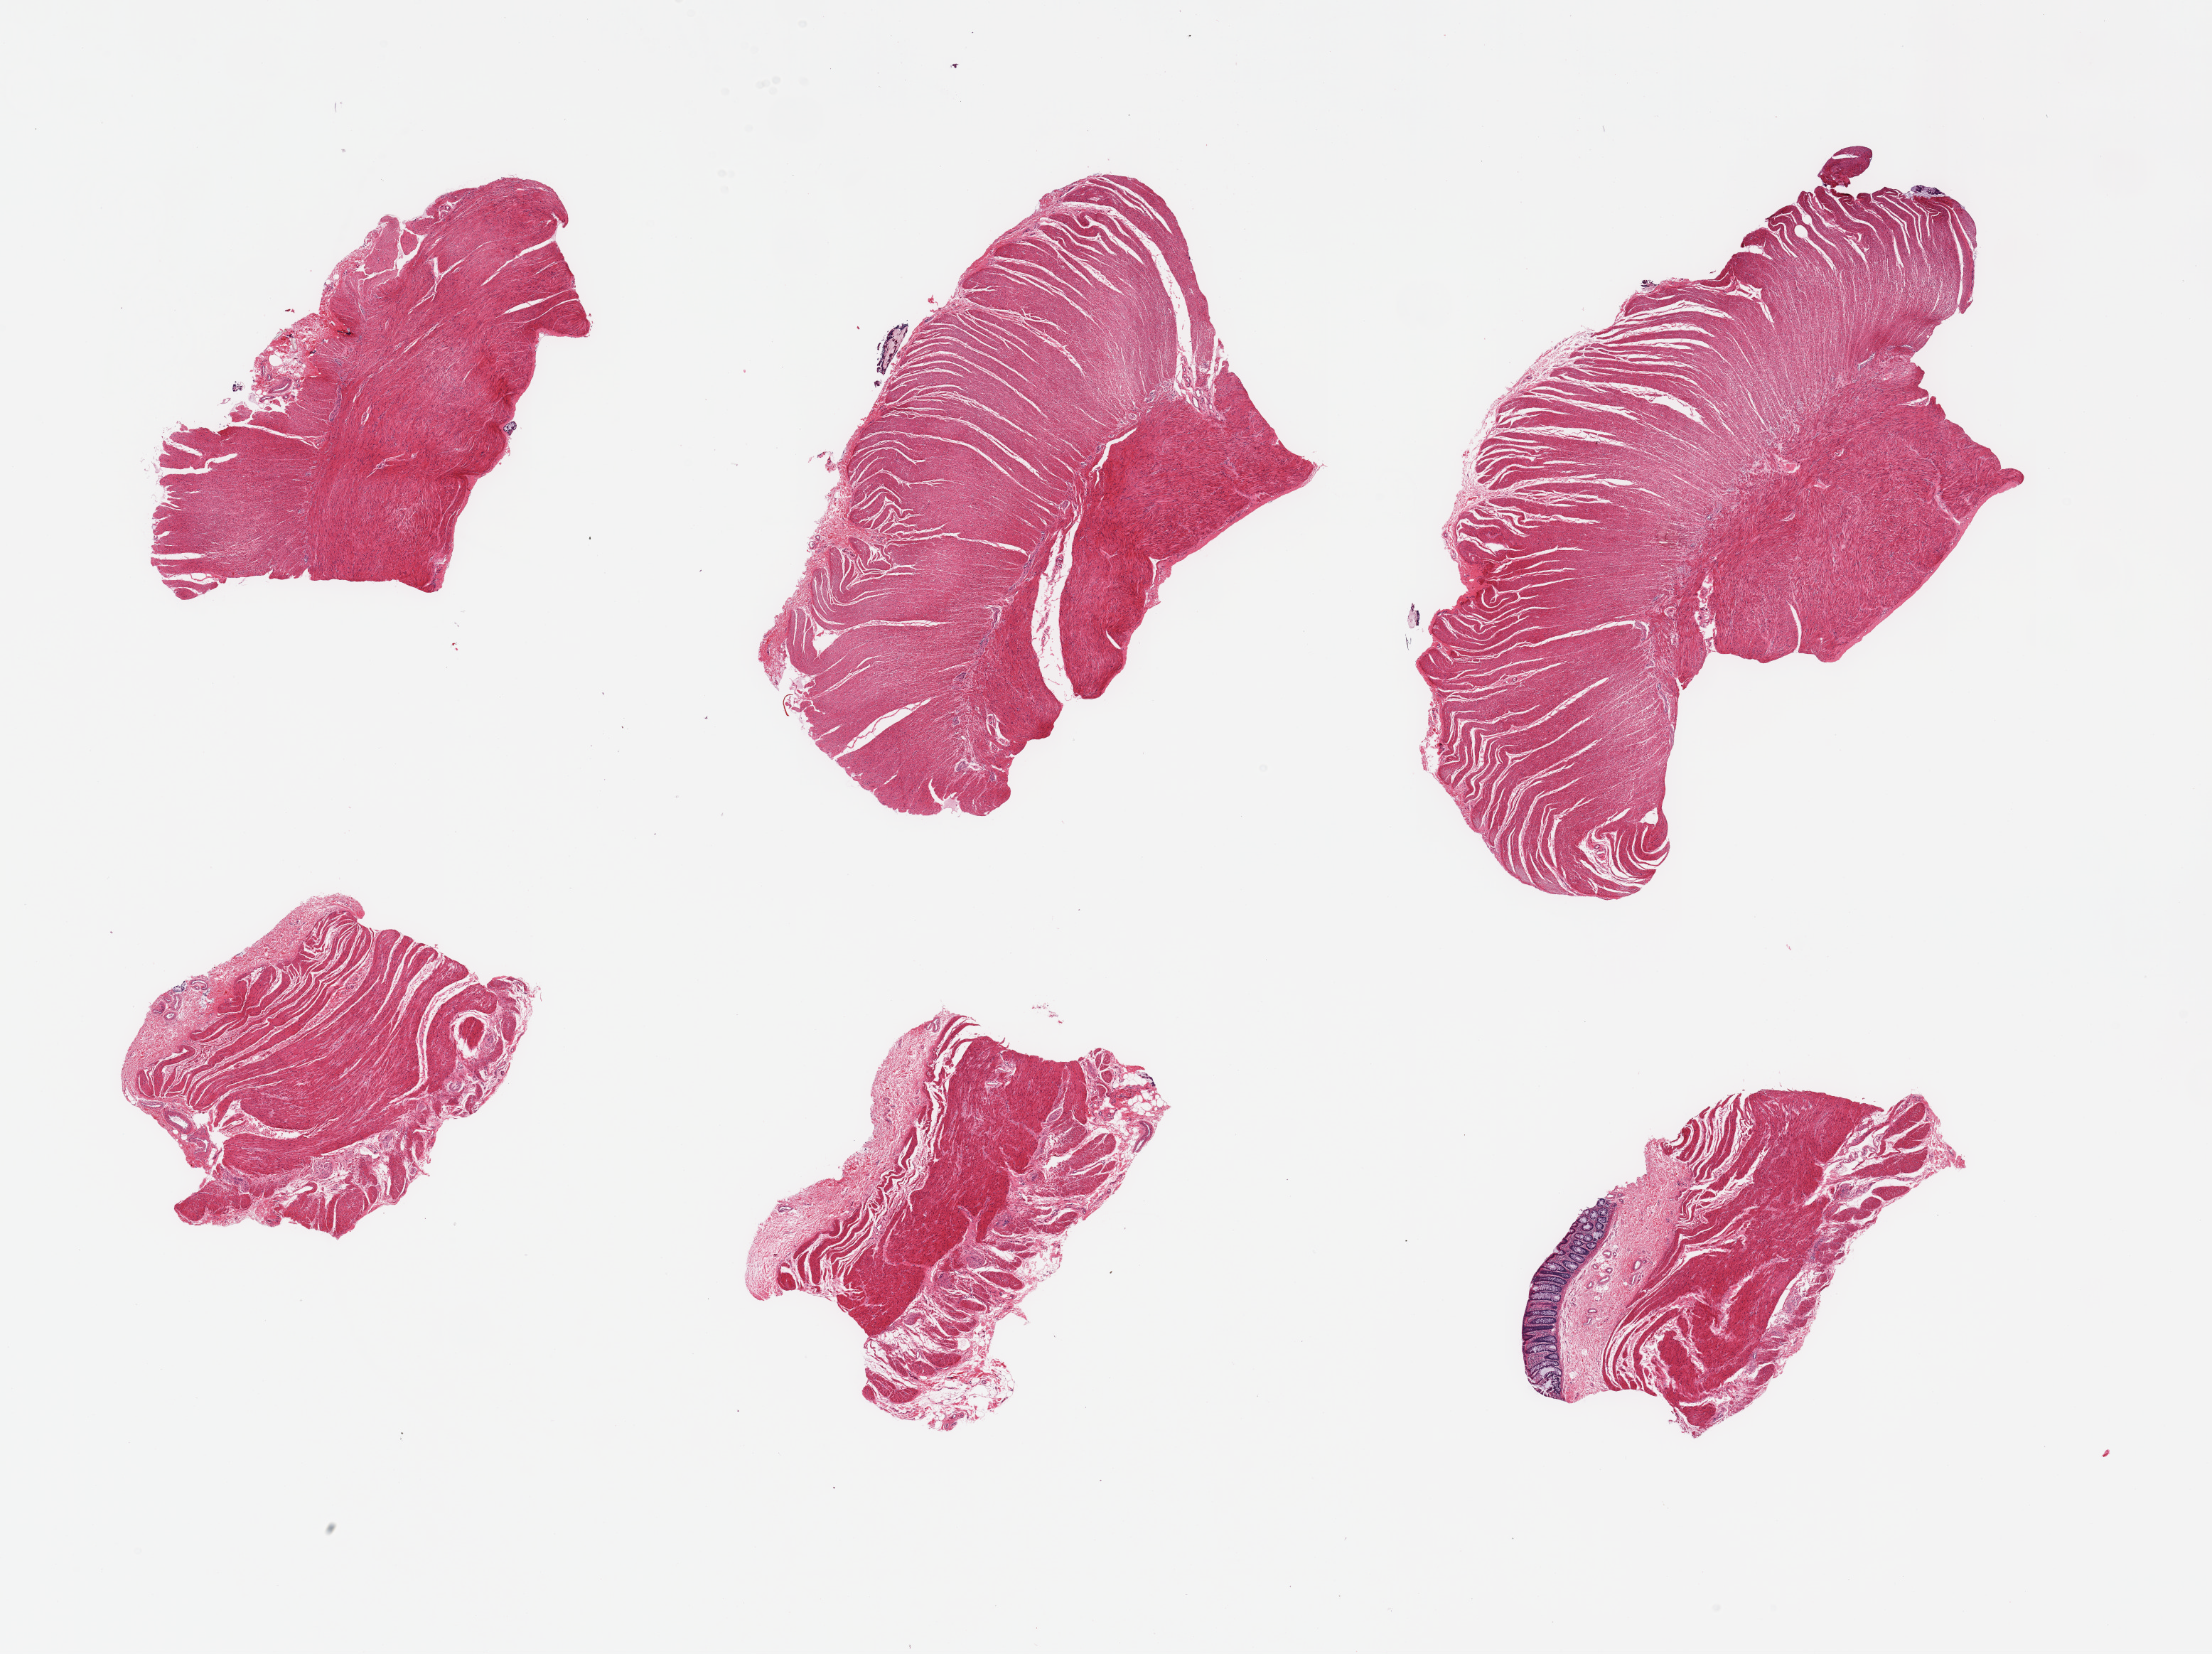
Digitized H&E-stained section, shown as a low-resolution overview of the whole scanned area (about 24.6 x 18.4 mm). PAXgene-fixed, paraffin-embedded tissue. Section of sigmoid colon (target tissue). Tissue donor sample.
Reviewer comment on this tissue sample: 2 pieces, confirmed target muscularis, focal 'contaminant' mucosa.